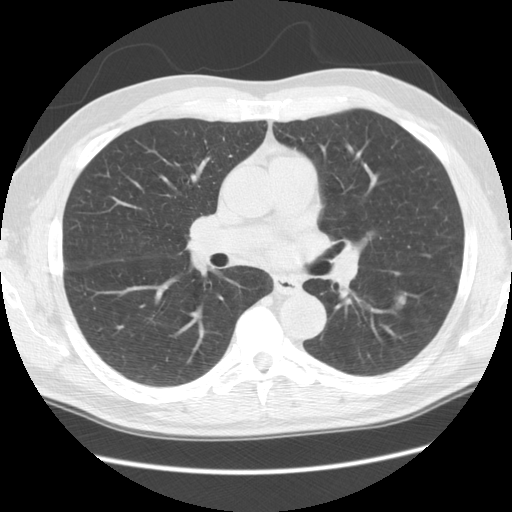
Low-dose screening chest CT, one axial slice; position 58 of 111 along the scan axis; lung window (W 1500 / L -600 HU); 2.5 mm slice thickness; 512 × 512 image matrix.
Annotated regions visible in this slice (expert manual segmentation):
- lesion 1 (tumor, lower lobe of left lung): bounding box (x1, y1, x2, y2) in pixels: (398, 295, 405, 305)